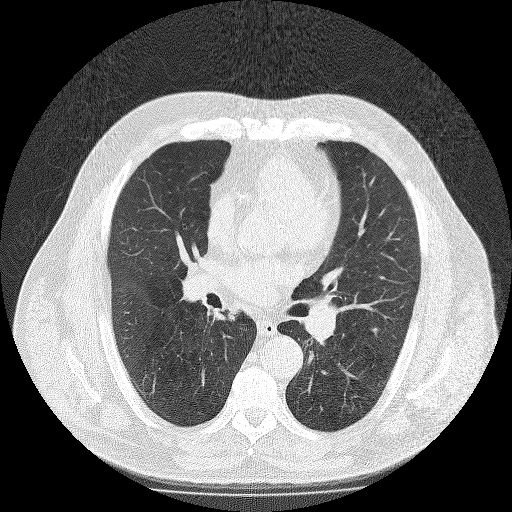
Chest CT (low-dose screening protocol), one axial image, second screening round (one year after baseline), lung window (W 1500 / L -600 HU), 2 mm slice thickness, slice 84 of 188 in the series, 512 × 512 image matrix, field of view 420 × 420 mm. Male, age 65 years at enrolment. Former smoker at enrolment.
Expert reader's lesion annotation, bounding box (x1, y1, x2, y2) in pixels: (207, 298, 251, 331). Screening reader's record for this exam (one nodule recorded; not confirmed to be the boxed lesion): non-calcified nodule or mass ≥4 mm, right lower lobe, 10 × 9 mm, spiculated (stellate) margins, soft tissue attenuation, pre-existing on the prior screen: yes; interval growth: no. Official screen result: positive, change unspecified: nodule(s) >= 4 mm or enlarging nodule(s), mass(es), or other non-specific abnormalities suspicious for lung cancer. Later outcome: lung cancer diagnosed 247 days after this screen — large cell neuroendocrine carcinoma, right lower lobe, undifferentiated (G4), stage IIIA (AJCC 6th edition).